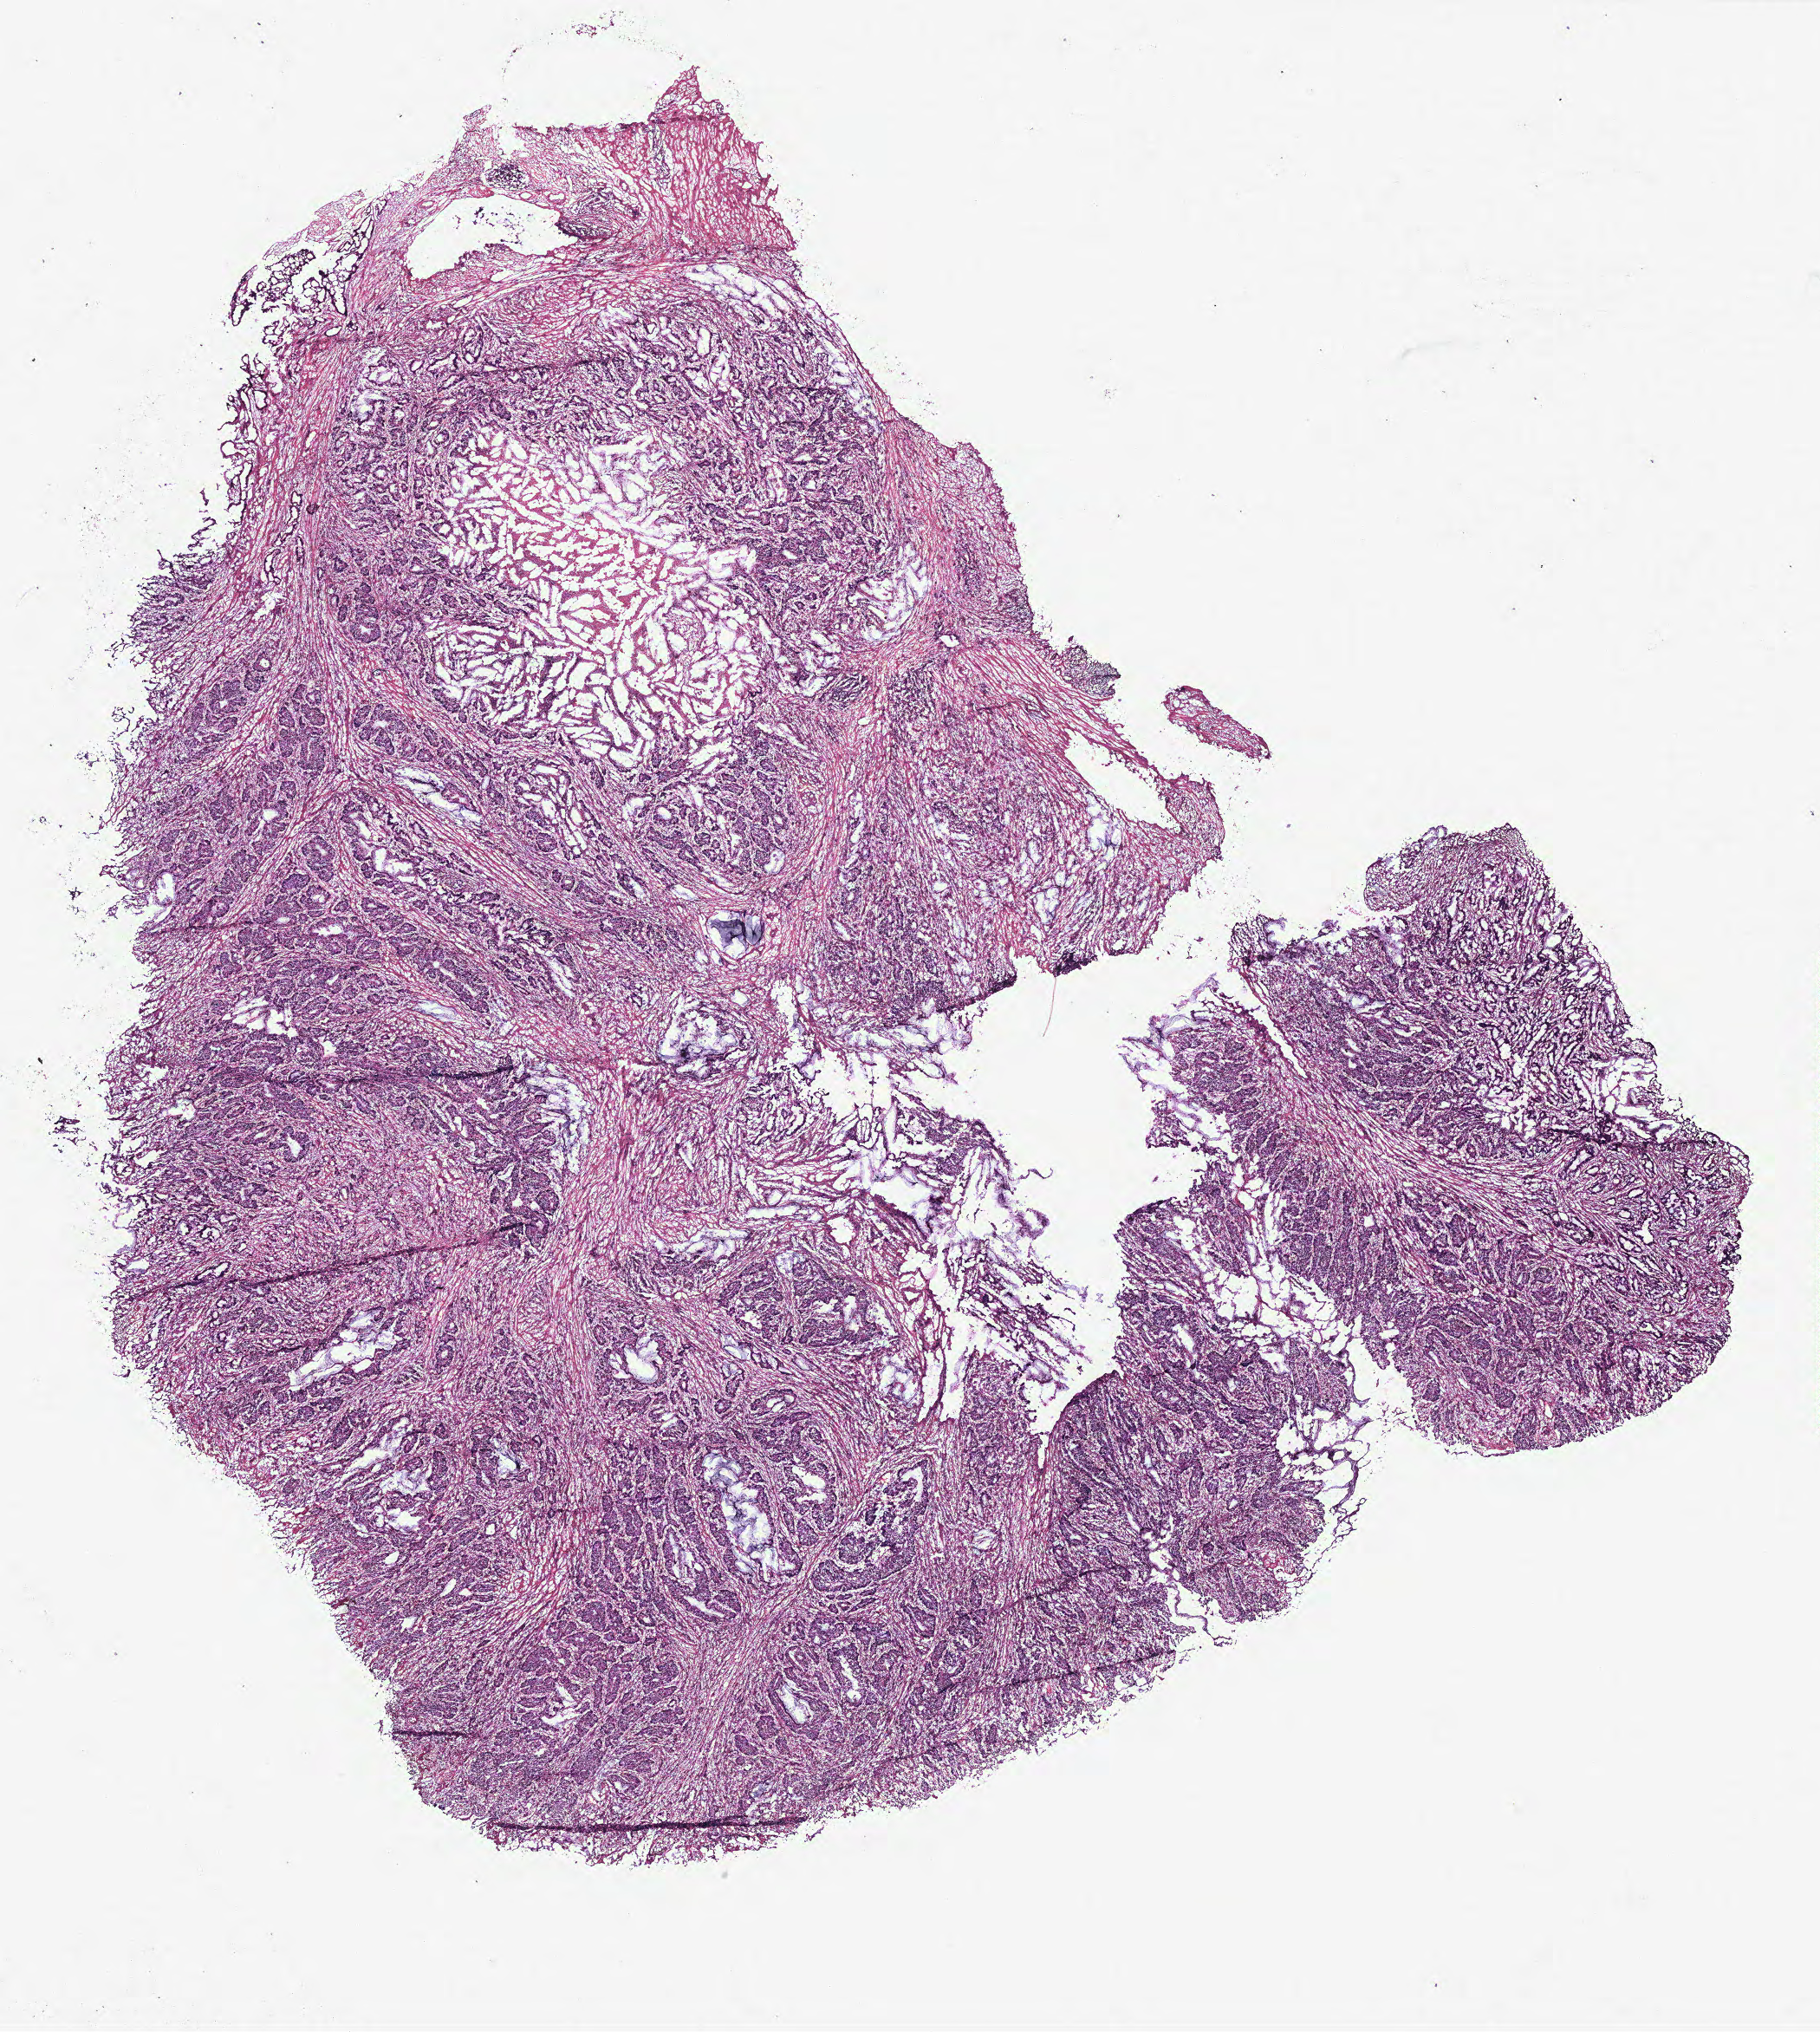
Whole-slide histology image, Hematoxylin and eosin (H&E) stained, low-resolution overview of the scanned area, about 16.8 x 18.8 mm (slide scanned at 40x); normal (non-tumour) tissue sample, colon. Female, 66 y/o.
This section: normal (non-tumour) tissue from the same patient. Patient diagnosis: Adenocarcinoma, NOS.